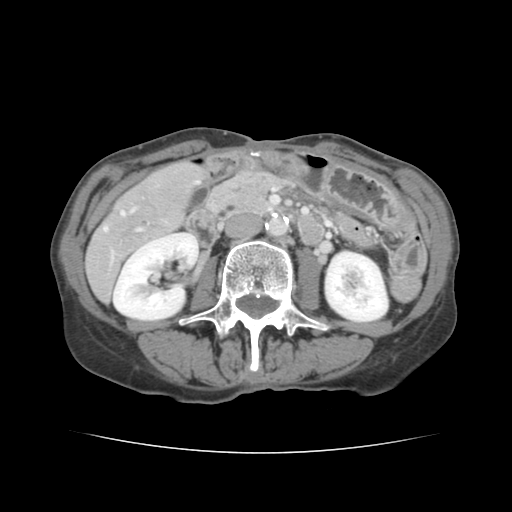
Contrast-enhanced abdominal CT, one axial slice; slice 46 of 136 in the series (ordered by position); 120 kVp; soft-tissue window (W 400 / L 40 HU); 2.5 mm slice thickness; 512 × 512 image matrix, field of view 319 × 319 mm. Female patient, age 77 years. From the clinical record (not read from this slice): diagnosis: colorectal cancer liver metastases, imaged before liver resection; multiple liver metastases: yes; largest metastasis: 3 cm; disease in both lobes: no.
Outlined on this slice (expert manual segmentation):
- hepatic veins: bounding box (x1, y1, x2, y2) in pixels: (104, 181, 198, 231)
- liver: (87, 162, 206, 299)
- planned liver remnant (the part of the liver to remain after resection): (172, 162, 206, 189)
- portal vein (with intrahepatic branches): (111, 228, 142, 258)